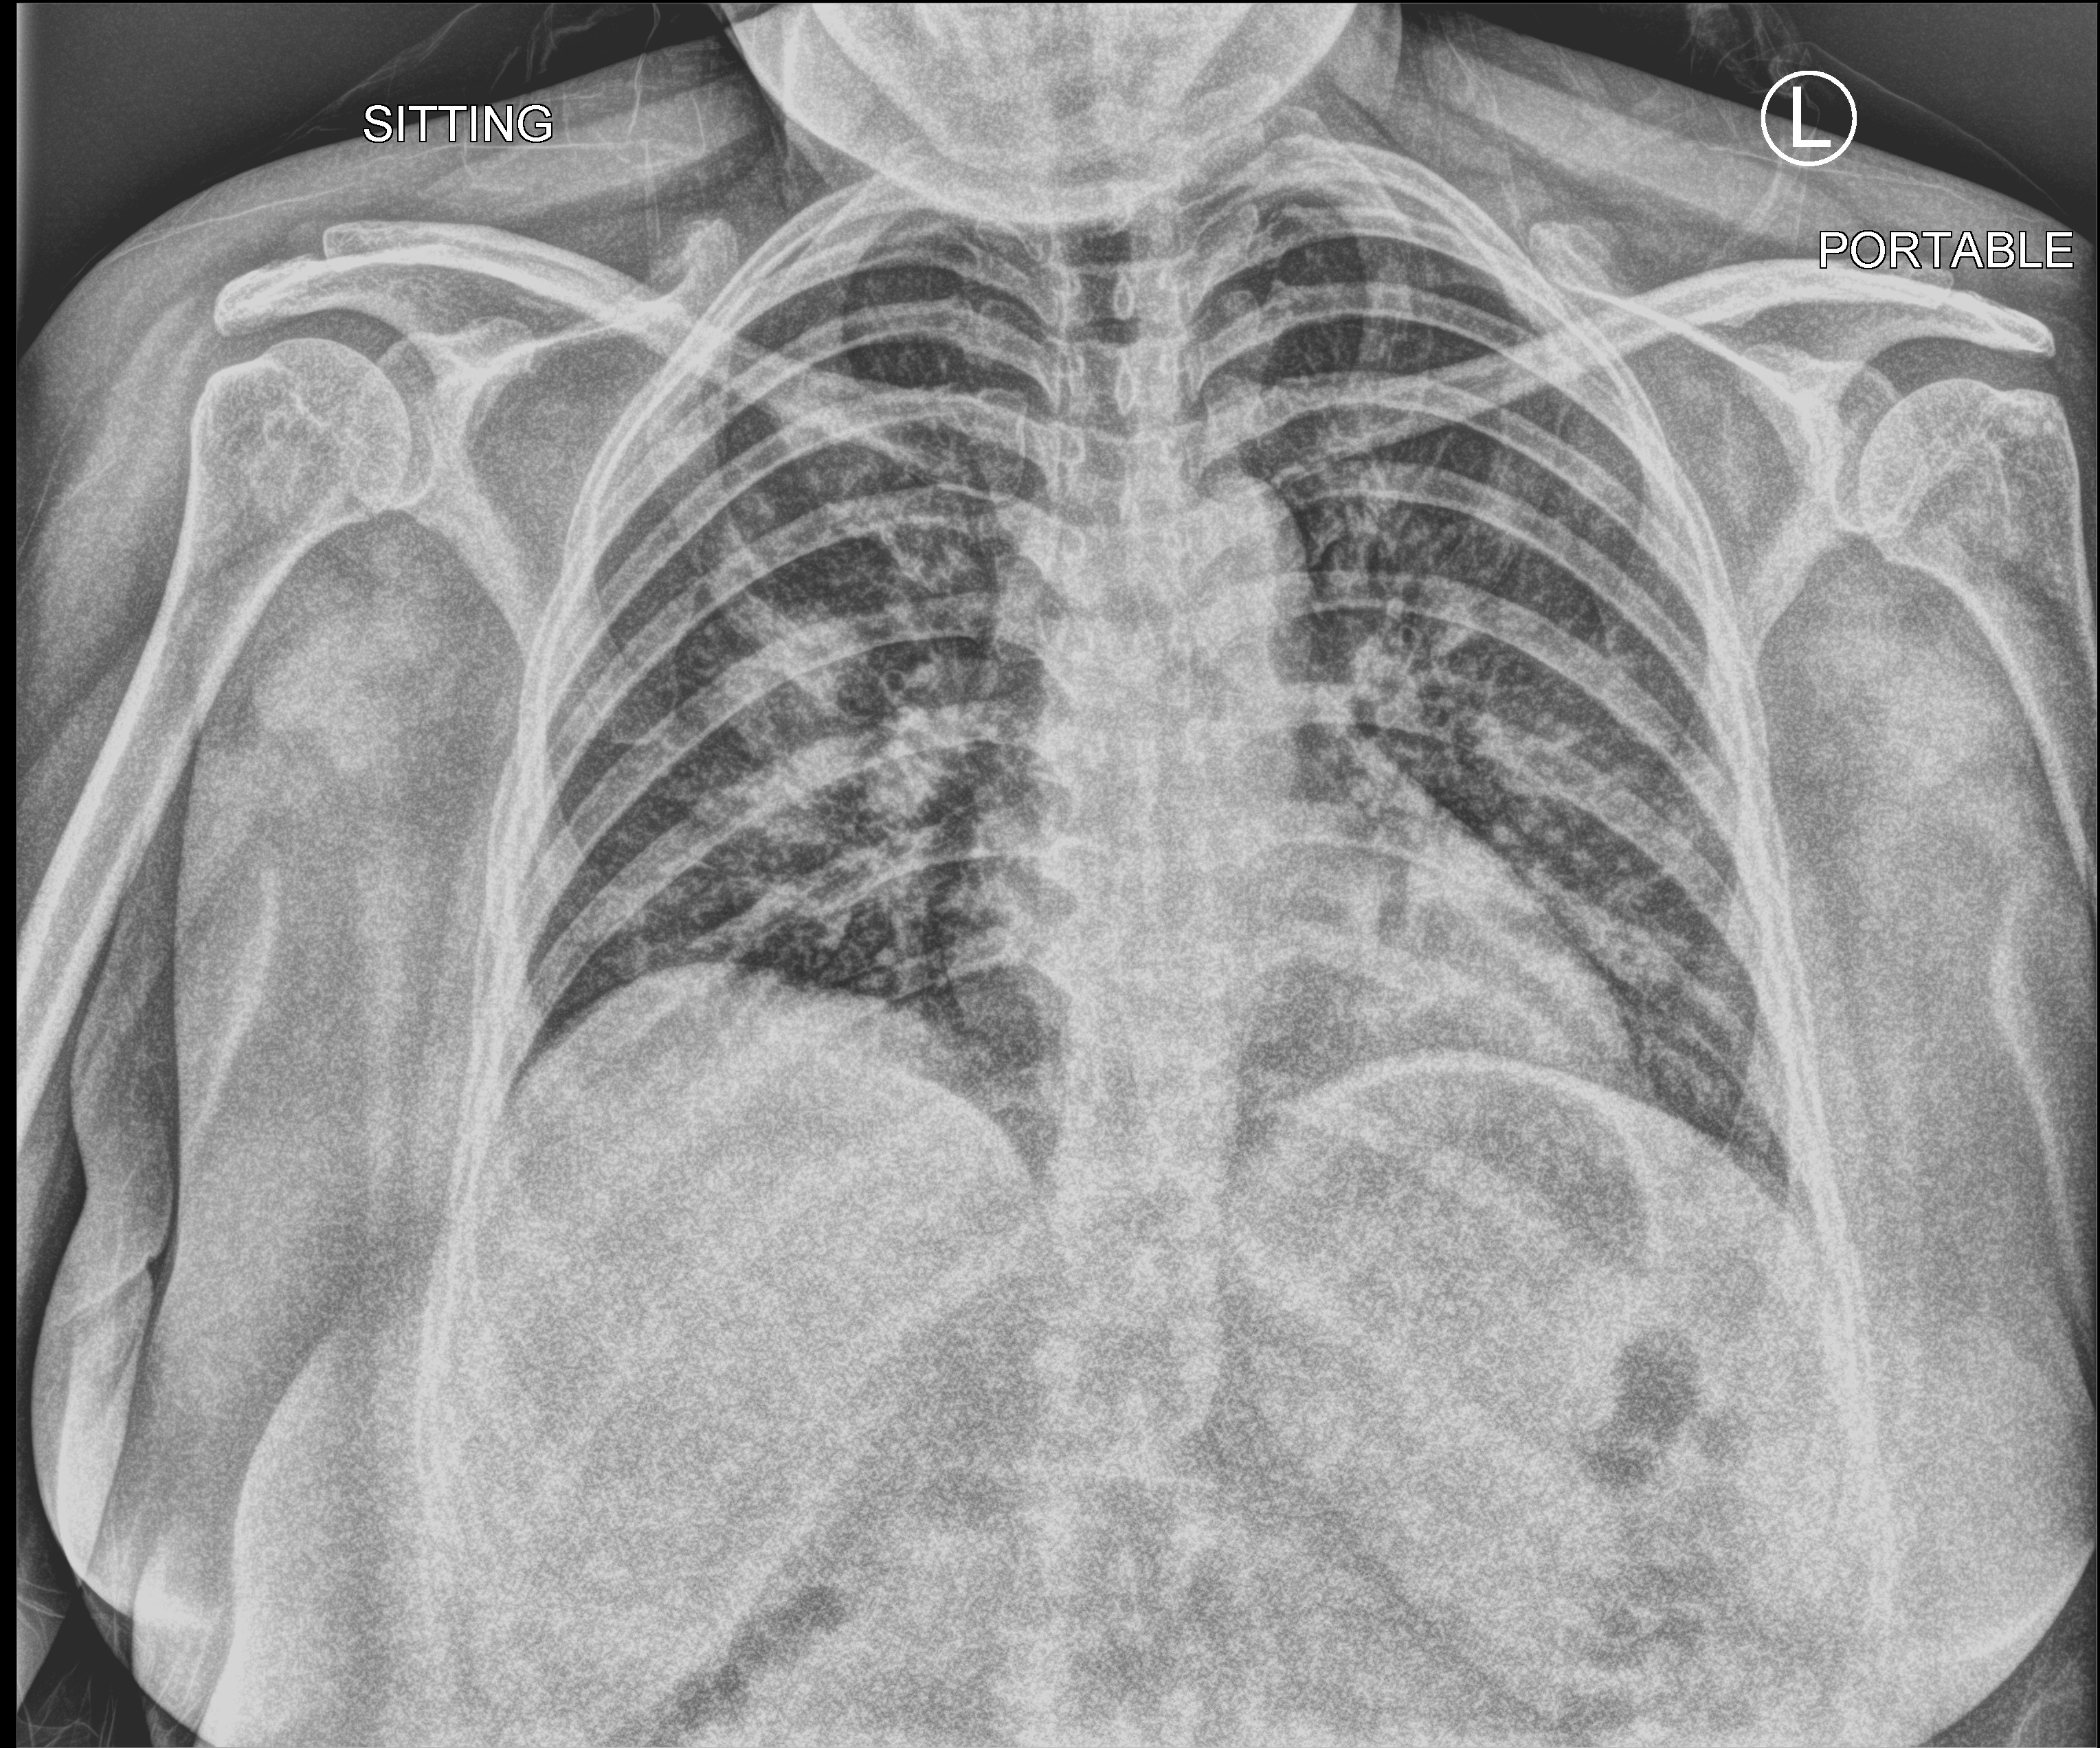
Bedside chest radiograph (computed radiography); anteroposterior (AP) projection. Female patient hospitalised with COVID-19, age 18–59 years.
Hospital-stay facts (about this admission, not read from this image; timing relative to this image not recorded): admitted to intensive care during this hospital stay: no.